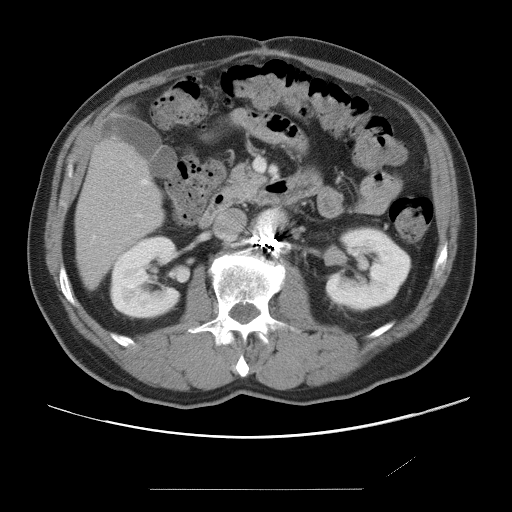
Contrast-enhanced abdominal CT, one axial slice. Slice 25 of 87 in the series (ordered by position). 120 kVp. Intravenous contrast given. Soft-tissue window (W 400 / L 40 HU). 5 mm slice thickness. 512 × 512 image matrix, field of view 406 × 406 mm. Male patient, age 74 years. From the clinical record (not read from this slice): diagnosis: colorectal cancer liver metastases, imaged before liver resection; multiple liver metastases: yes; largest metastasis: 1.1 cm; disease in both lobes: no.
Annotated regions visible in this slice (expert manual segmentation):
- hepatic veins: bounding box <93,180,148,238> (left, top, right, bottom; pixels)
- liver: <76,142,161,287>
- planned liver remnant (the part of the liver to remain after resection): <76,142,161,287>
- portal vein (with intrahepatic branches): <138,214,142,217>